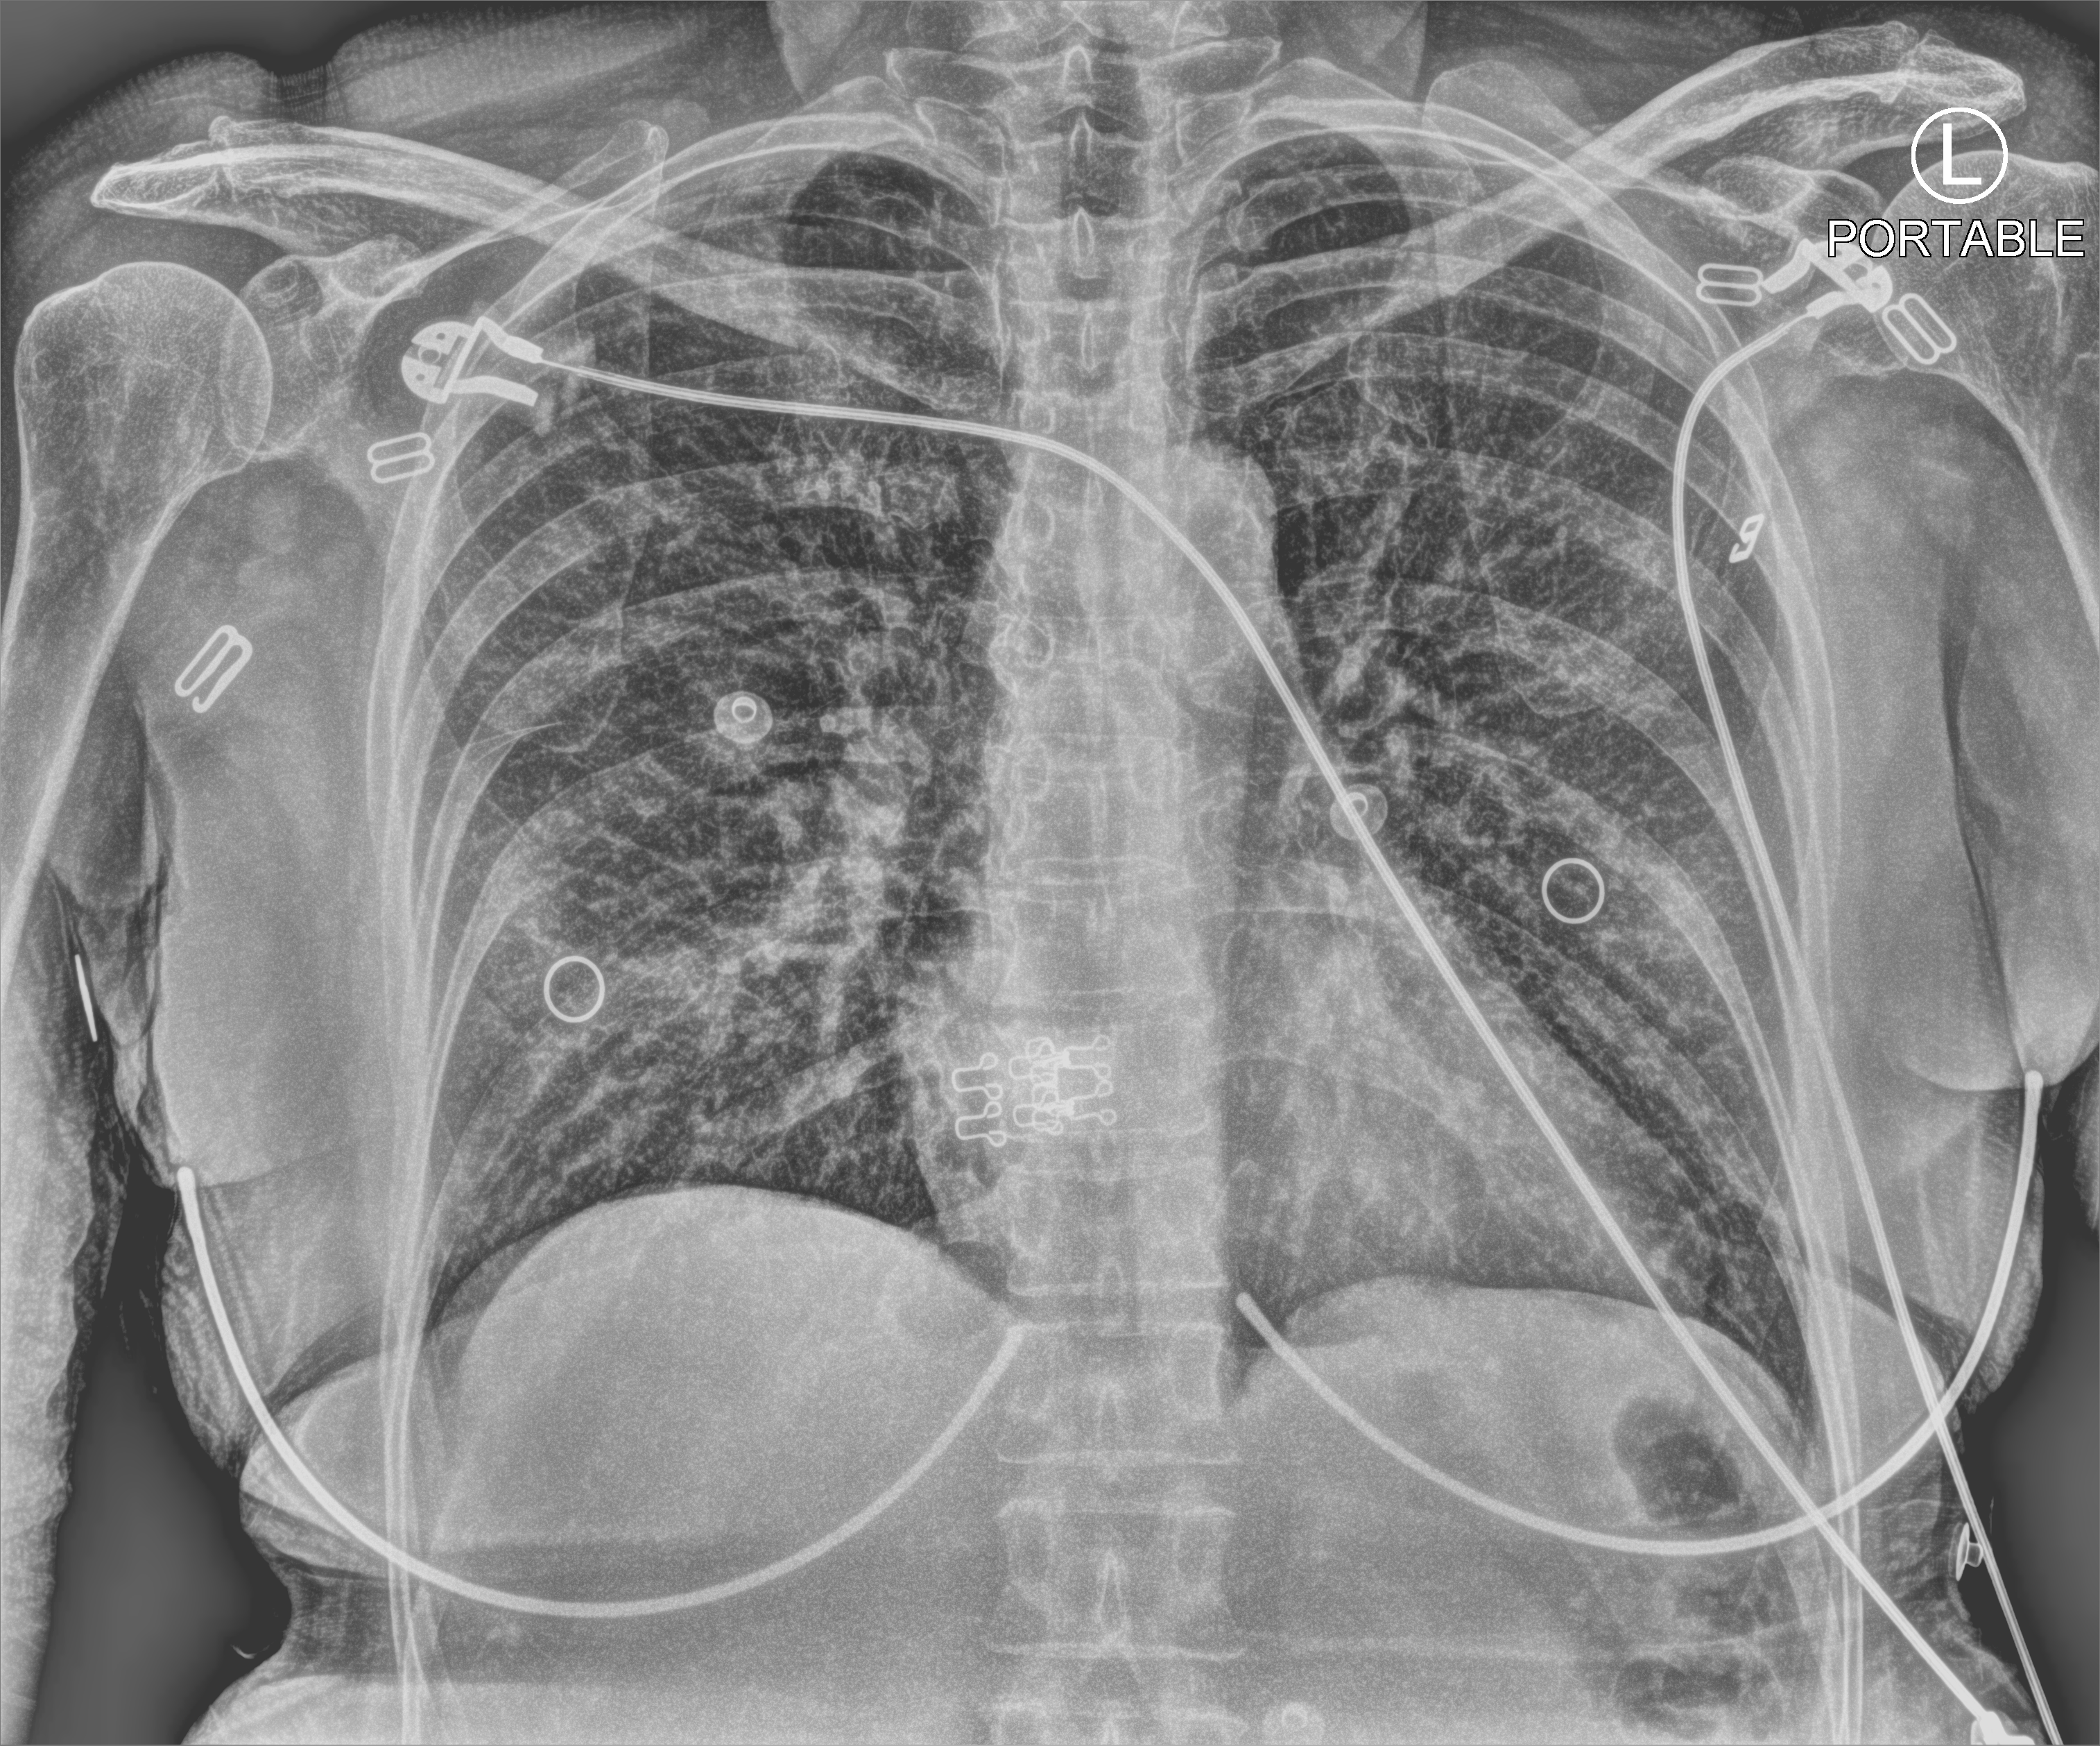
Chest X-ray (portable). Patient hospitalised with COVID-19; female, aged 60–74 years.
From the hospital-stay record, not from the radiograph (when in the stay this image was taken is not recorded): mechanically ventilated during this hospital stay: no.